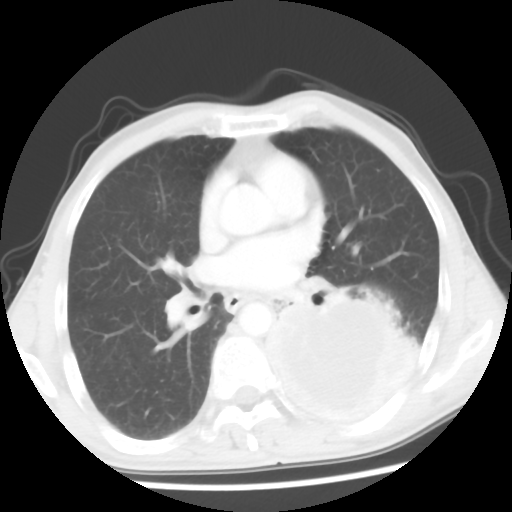
Chest CT, one axial slice. Position 29 of 56 along the scan axis. Reconstruction kernel STANDARD. 120 kVp. Lung window (W 1500 / L -600 HU). 5 mm slice thickness. 512 × 512 image matrix, field of view 318 × 318 mm. Male patient, age 60 years. Case-level facts recorded for this patient, not image findings: clinical TNM (as recorded): T4 N0 M0.
Outlined on this slice (rectangle marked by the reading radiologist):
- lung tumour (recorded histology: squamous cell carcinoma): bounding box <260,292,427,436> (left, top, right, bottom; pixels)